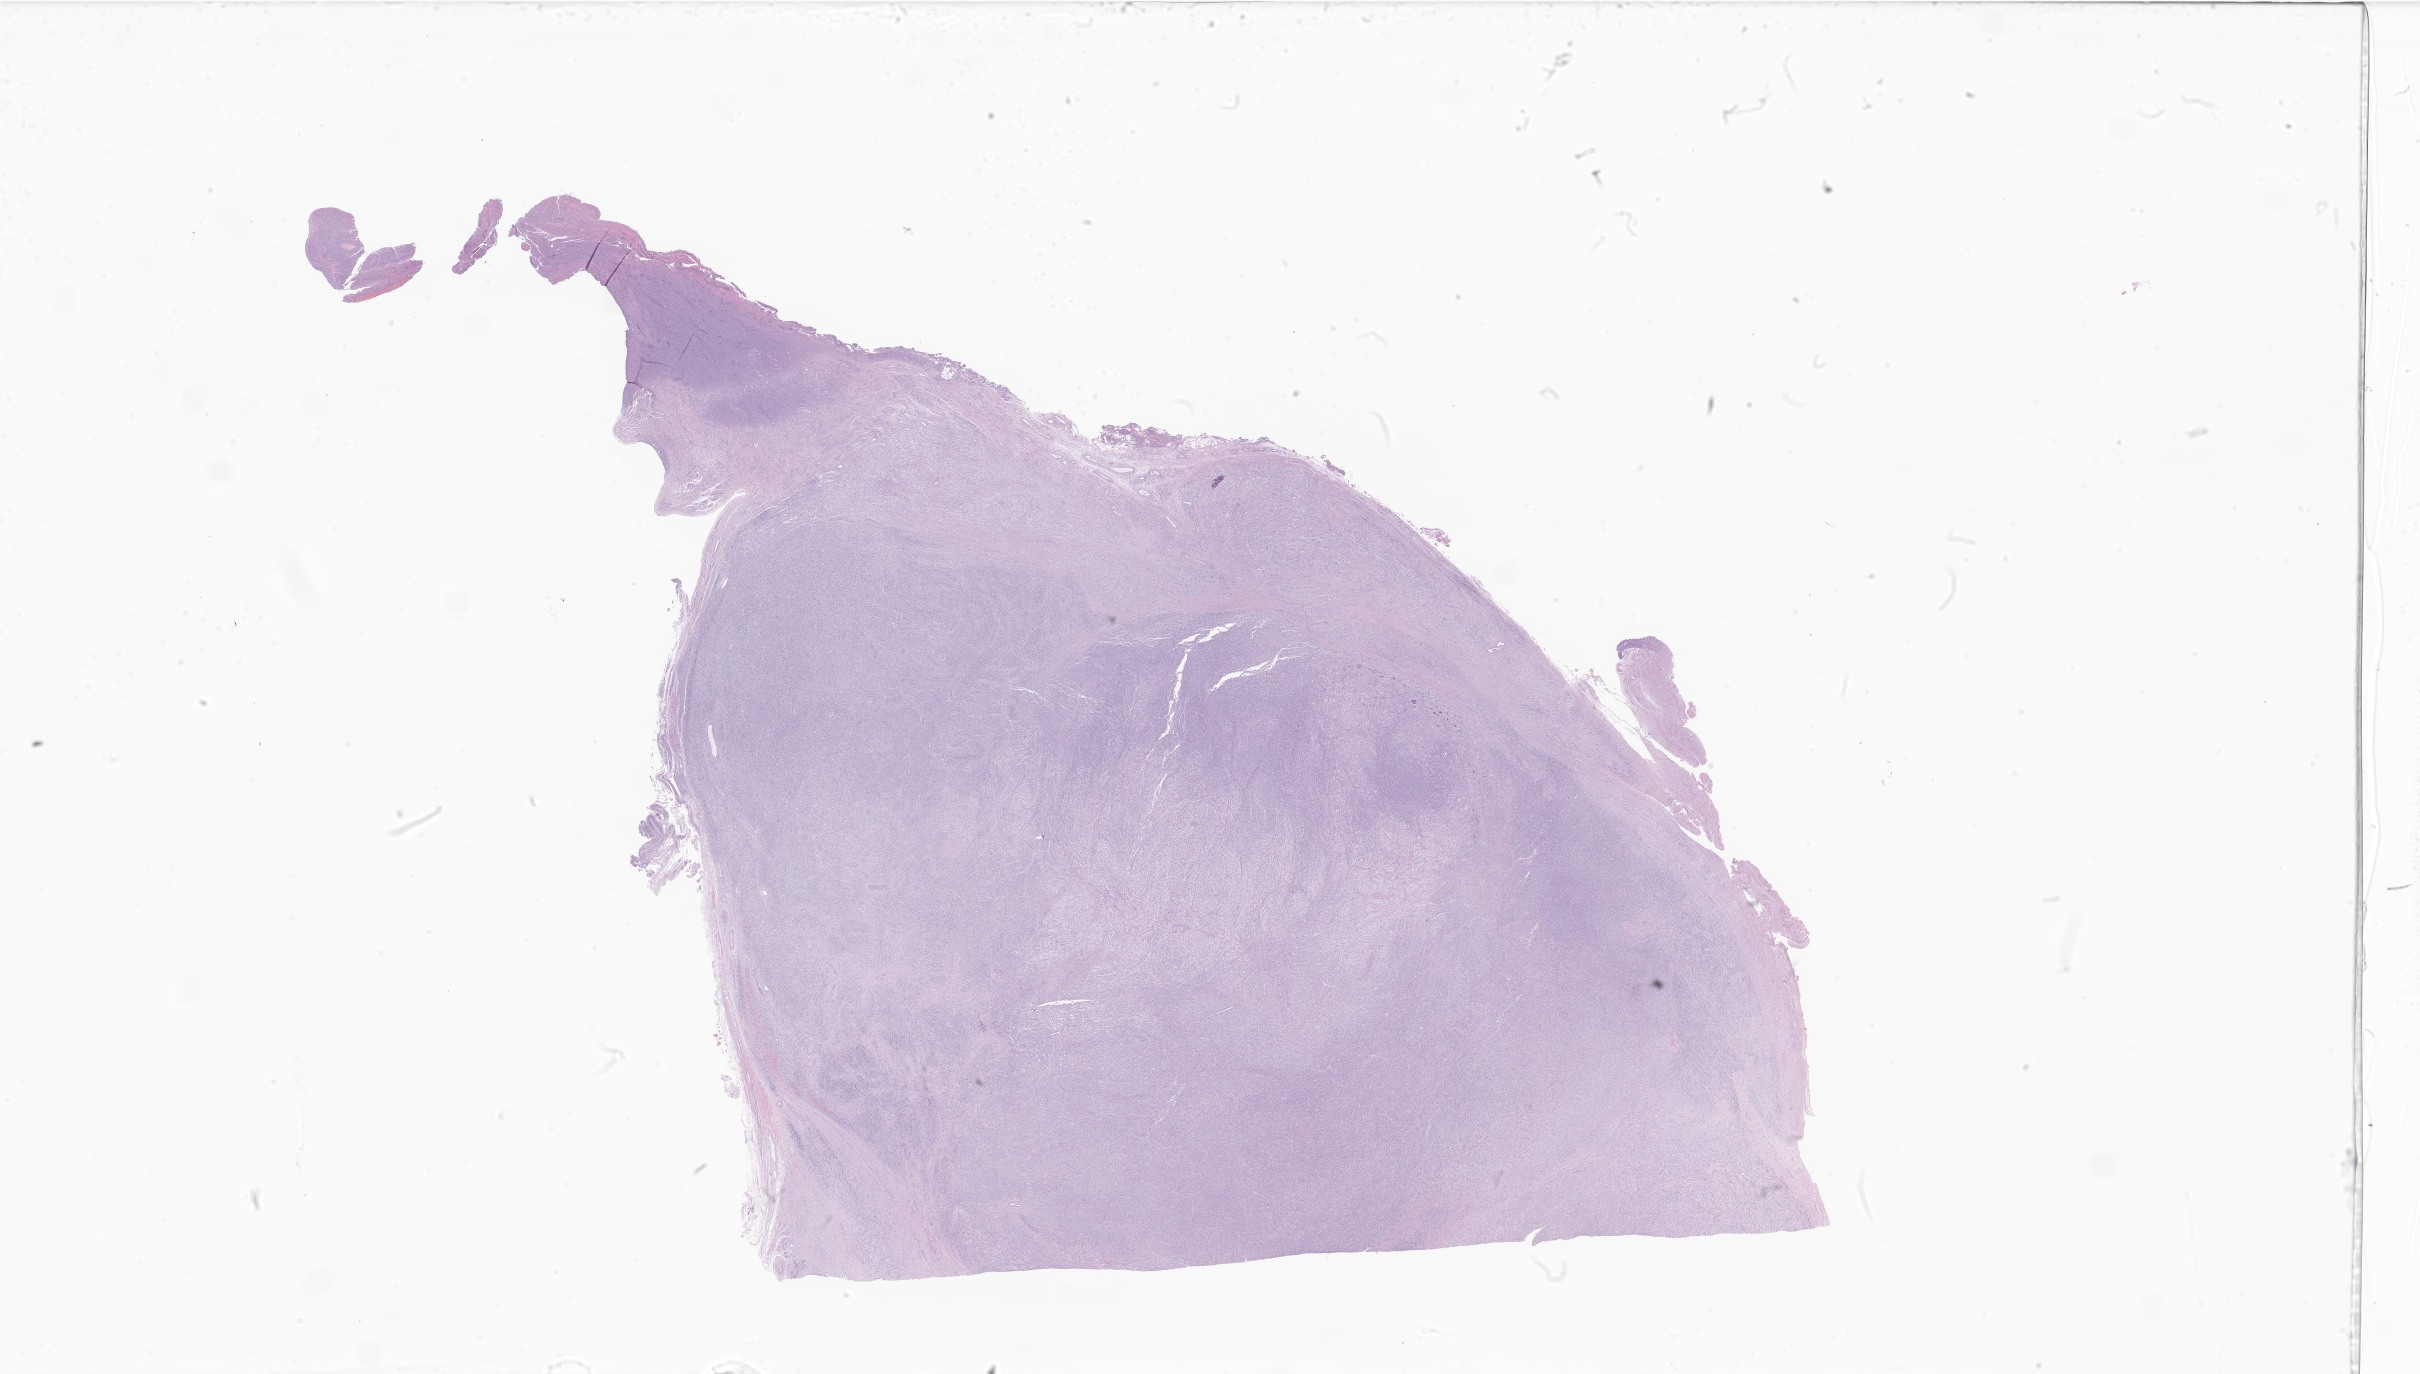
Whole-slide image, H&E stain of tumor tissue from the soft tissue of pelvis, a low-resolution overview of the entire scanned area, about 40.8 x 23.2 mm; formalin-fixed, paraffin-embedded (FFPE) tissue. Patient: female, age 371 days (about 1.0 years).
* recorded diagnosis: Embryonal rhabdomyosarcoma, NOS
* tissue or organ of origin (case record): connective, subcutaneous and other soft tissues of pelvis